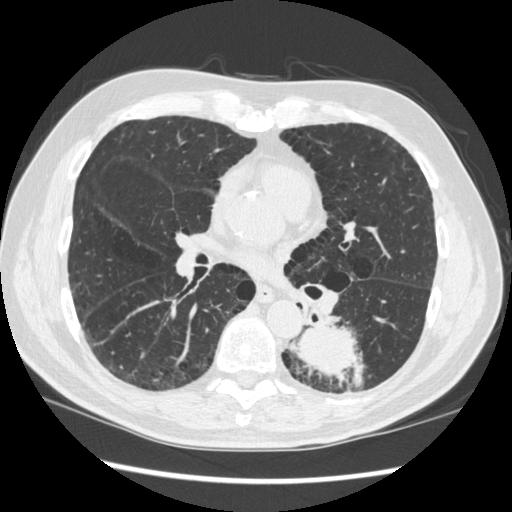
Axial slice from a low-dose chest CT screening exam, first (baseline) screen, lung window (W 1500 / L -600 HU), 1.25 mm slice thickness, standard (soft-tissue) reconstruction kernel (STANDARD), 120 kVp, 512 × 512 image matrix, field of view 360 × 360 mm. Male participant, aged 72 years at enrolment. Current smoker at enrolment.
• Expert reader's lesion annotation, bounding box (x1, y1, x2, y2) in pixels: (265, 305, 369, 398).
• The screening reader recorded 2 non-calcified nodules or masses ≥4 mm on this exam; which of them this box marks is not recorded.
• Official screen result: positive, change unspecified: nodule(s) >= 4 mm or enlarging nodule(s), mass(es), or other non-specific abnormalities suspicious for lung cancer.
• Lung cancer was diagnosed 37 days after this screen: squamous cell carcinoma, NOS, left lower lobe, stage IIIA (AJCC 6th edition), 60 mm at pathology.